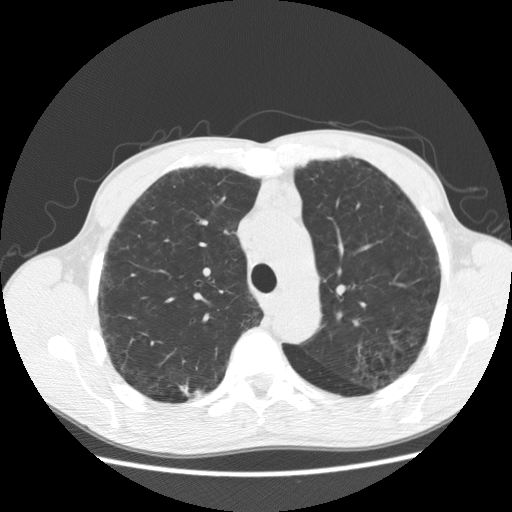
Low-dose screening chest CT, axial slice; second annual screen; lung window (W 1500 / L -600 HU); standard (soft-tissue) reconstruction kernel (STANDARD); 120 kVp; slice 139 of 195 in the series; 512 × 512 image matrix. Male participant, aged 60 years at enrolment. Current smoker at enrolment.
• Expert reader's lesion annotation, box from (x=170, y=376) to (x=212, y=408) px.
• The exam's reader record, not a measurement of the box and not confirmed to be the same lesion: non-calcified nodule or mass ≥4 mm, right upper lobe, 8 × 5 mm, poorly defined margins, soft tissue attenuation, pre-existing on the prior screen: yes; interval growth: yes.
• Official screen result: positive, other.
• Later outcome: lung cancer diagnosed 204 days after this screen — squamous cell carcinoma, NOS, right upper lobe, well differentiated (G1), stage IA (AJCC 6th edition), 15 mm at pathology.